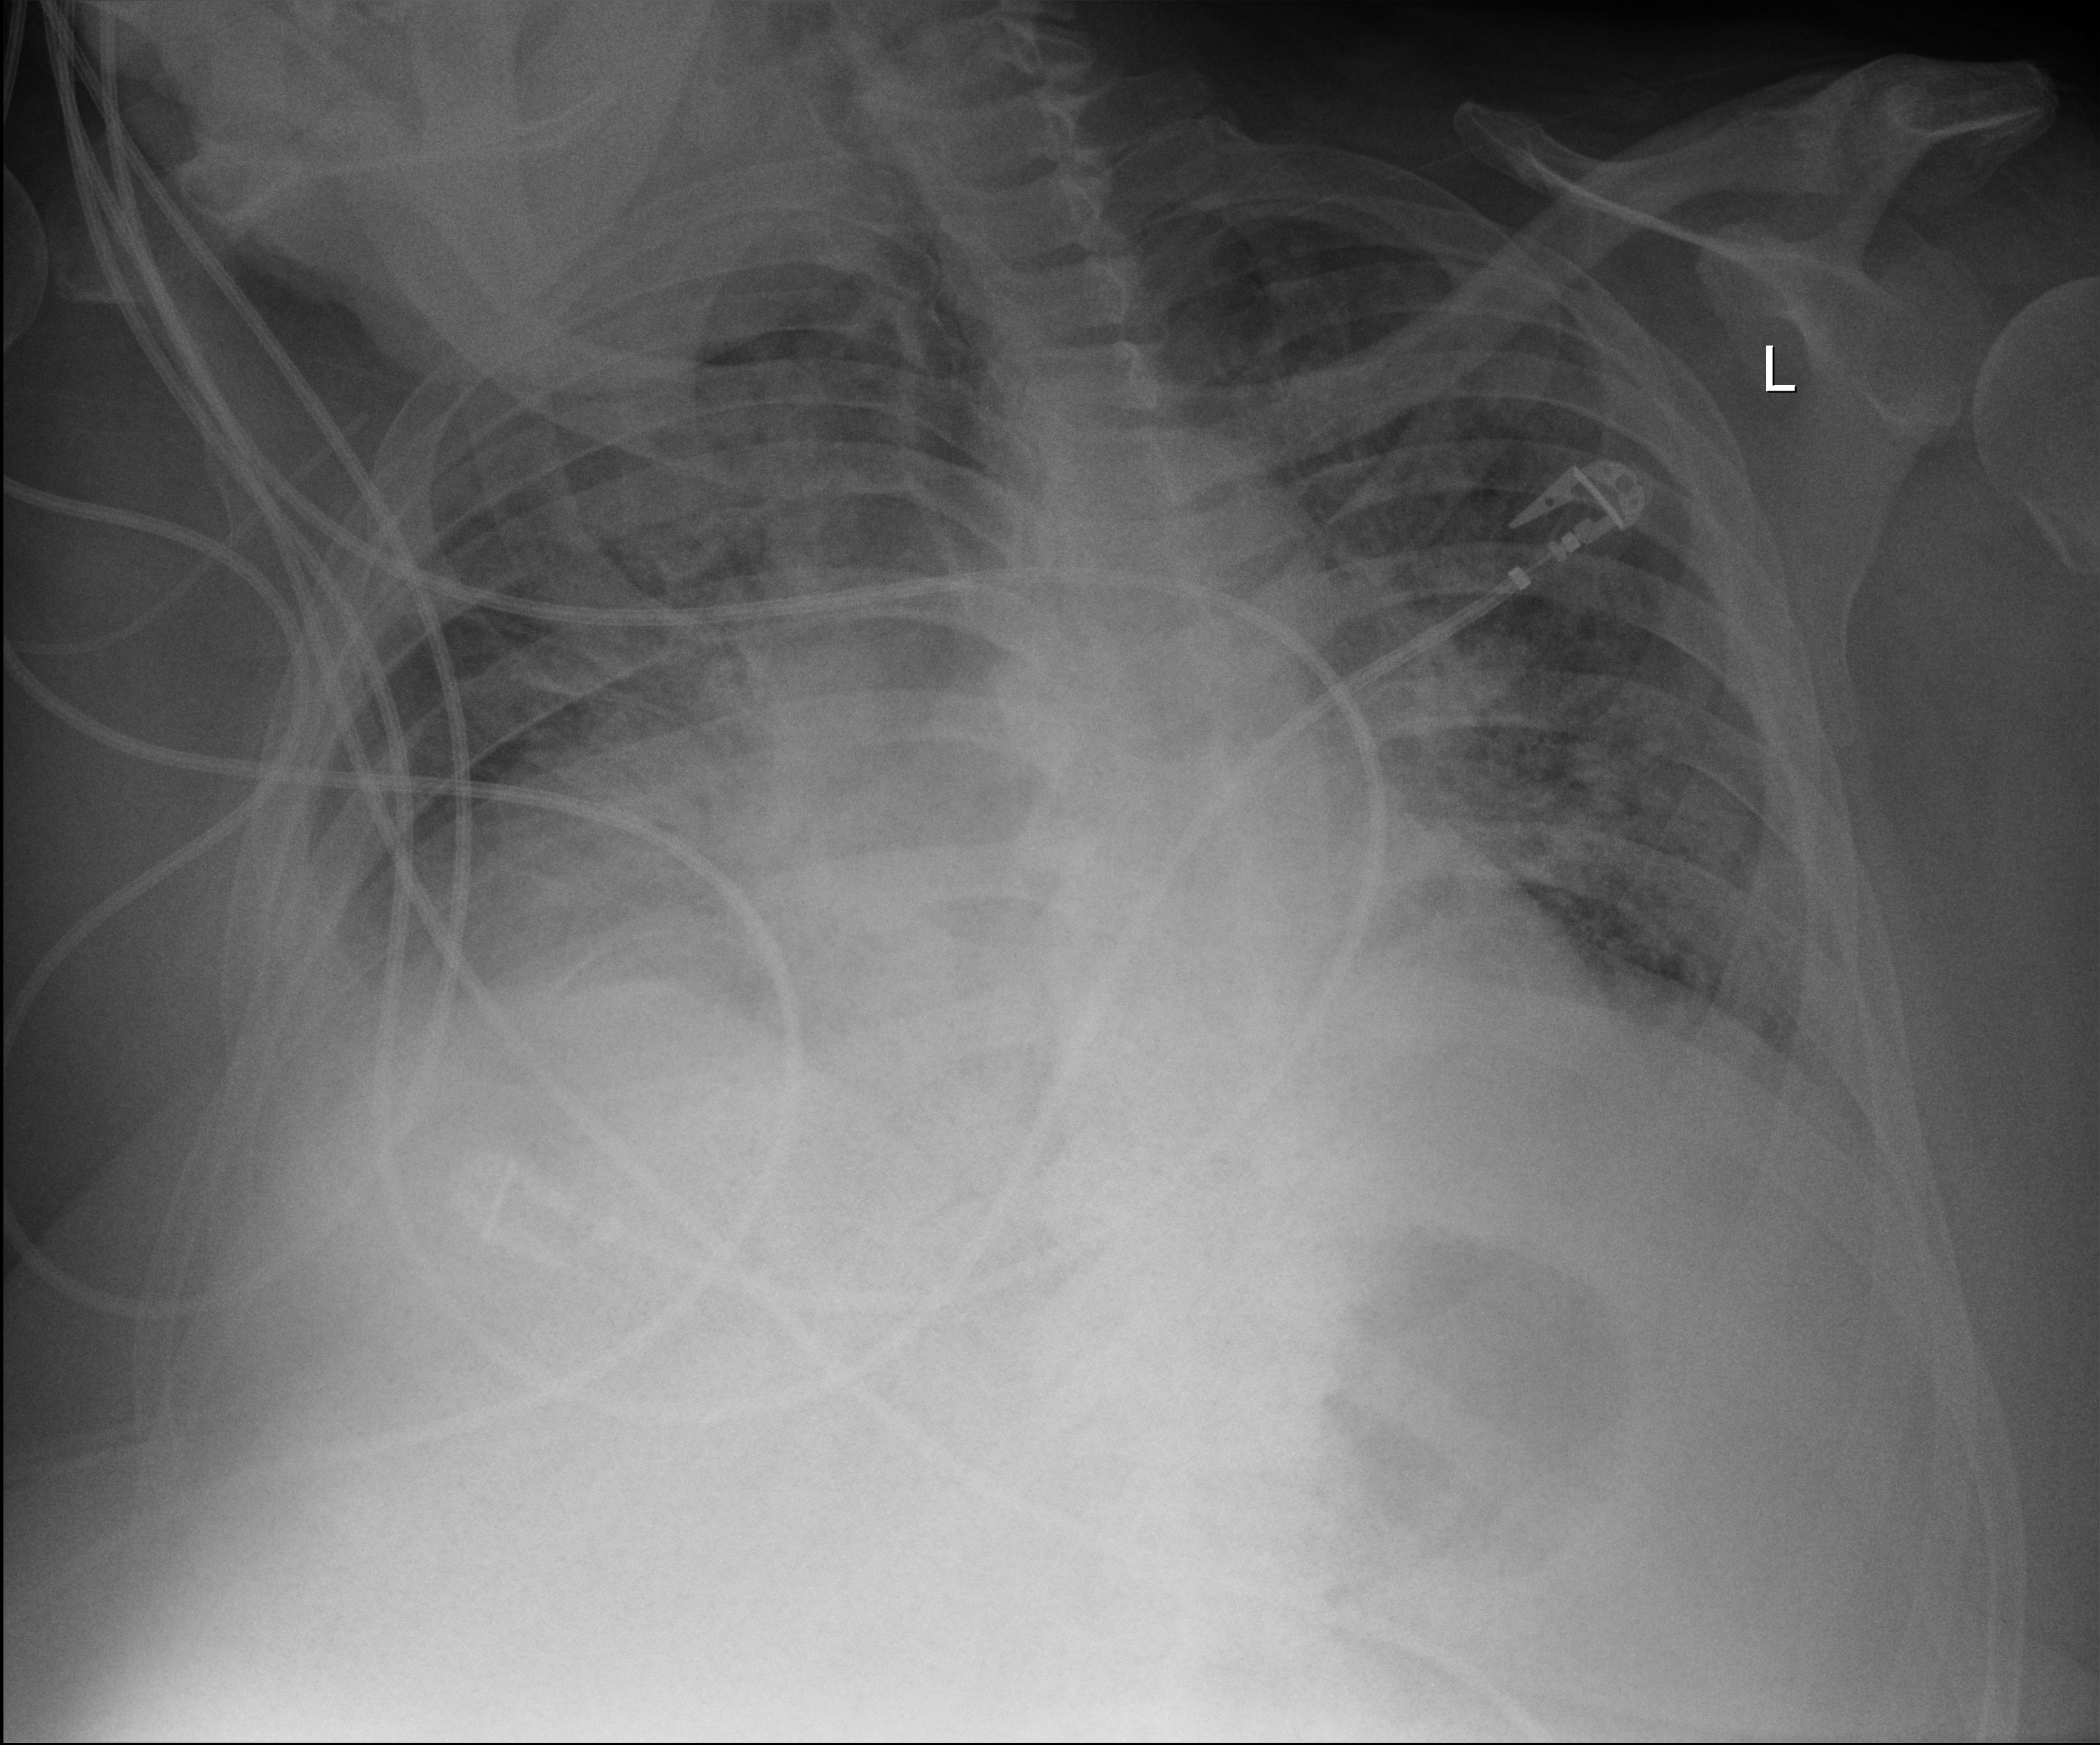
Chest X-ray (portable). Male patient hospitalised with COVID-19, age 60–74 years.
Hospital-stay facts (about this admission, not read from this image; timing relative to this image not recorded): hypertension (admission record): yes.